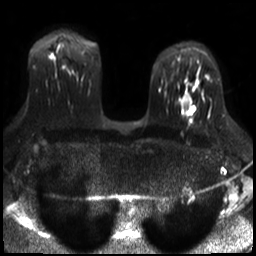
Breast MRI, one axial slice; position 20 of 30 along the scan axis; diffusion-weighted series; image 2 of 4 stored at this slice position (different b-values; order by instance number); 3 T; 4 mm slice thickness; 256 × 256 image matrix, field of view 320 × 320 mm. Female patient.
Structures marked on this image (manually delineated by an expert):
- tumour on diffusion-weighted imaging: bounding box <182,94,191,101> (left, top, right, bottom; pixels)